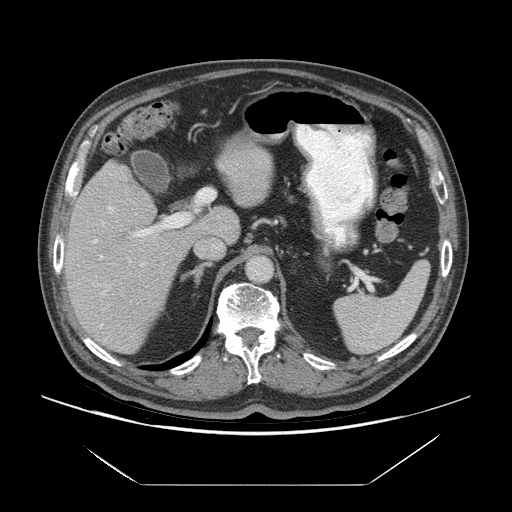
Contrast-enhanced abdominal CT (liver protocol), one axial slice. Position 40 of 75 along the scan axis. Reconstruction kernel STANDARD. 140 kVp. Soft-tissue window (W 400 / L 40 HU). 2.5 mm slice thickness. 512 × 512 image matrix, field of view 420 × 420 mm. Case-level facts recorded for this patient, not image findings: diagnosis: hepatocellular carcinoma (patient treated with transarterial chemoembolisation; whether this scan precedes or follows treatment is not stated here); TNM stage (as recorded): Stage-I; Child-Pugh class: A; tumour nodularity: uninodular.
Structures marked on this image (semi-automatically segmented with operator editing):
- liver parenchyma outside the tumour (the mass and vessels are separate outlines, so this box may not span the whole liver): bounding box [x1, y1, x2, y2] px = [64, 160, 239, 353]
- liver vessels: [92, 206, 191, 328]